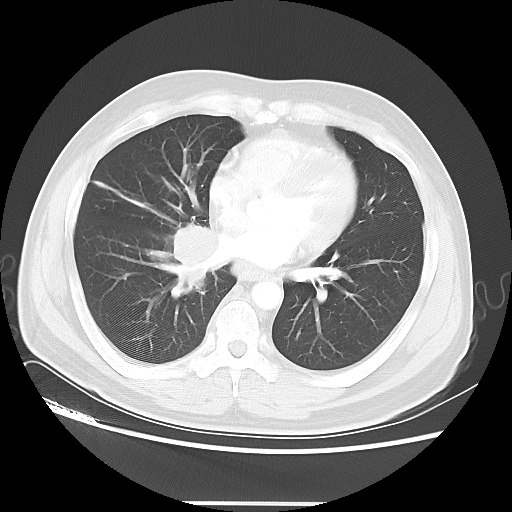
Chest CT, one axial slice; slice 19 of 48 in the series (ordered by position); 120 kVp; lung window (W 1500 / L -600 HU); 5 mm slice thickness; 512 × 512 image matrix, field of view 390 × 390 mm. Male patient, age 53 years. Case-level facts recorded for this patient, not image findings: clinical TNM (as recorded): T2 N3 M0.
Annotated regions visible in this slice (bounding box drawn by a radiologist):
- lung tumour (recorded histology: small cell carcinoma): bounding box (x1, y1, x2, y2) in pixels: (171, 226, 222, 286)